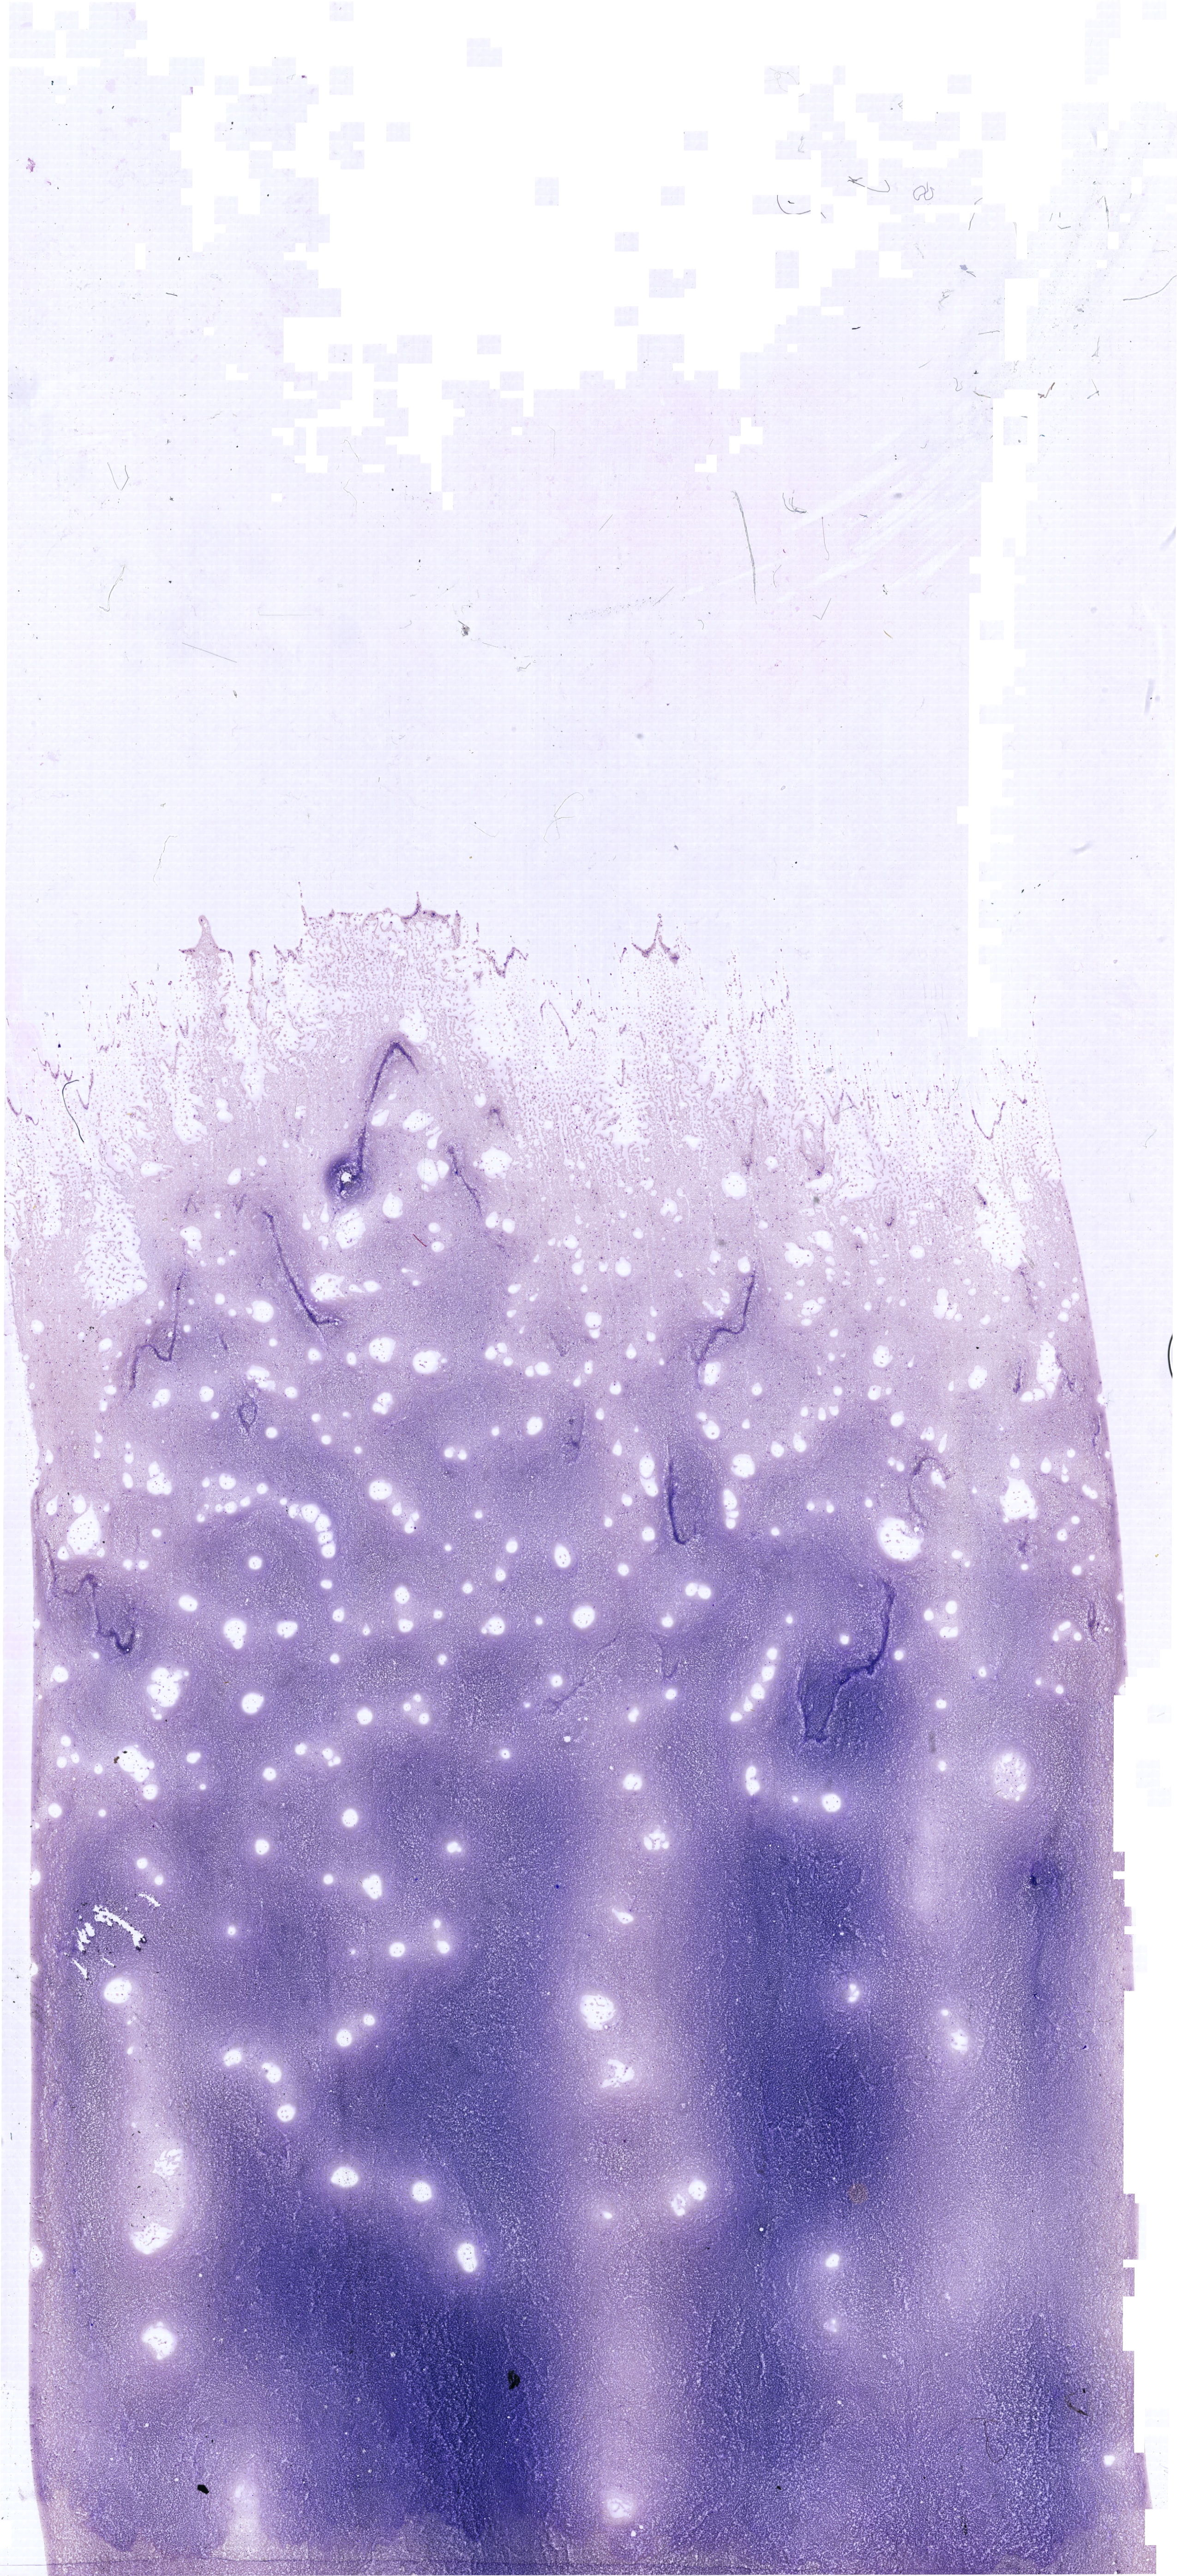
Bone marrow aspirate smear, May-Grünwald-Giemsa (MGG) stain, whole-slide image — shown as a low-resolution overview of the whole scanned area (about 19.9 x 43.6 mm). Patient sex: male.
Diagnosis: Mixed Phenotype Acute Leukemia, B/Myeloid.